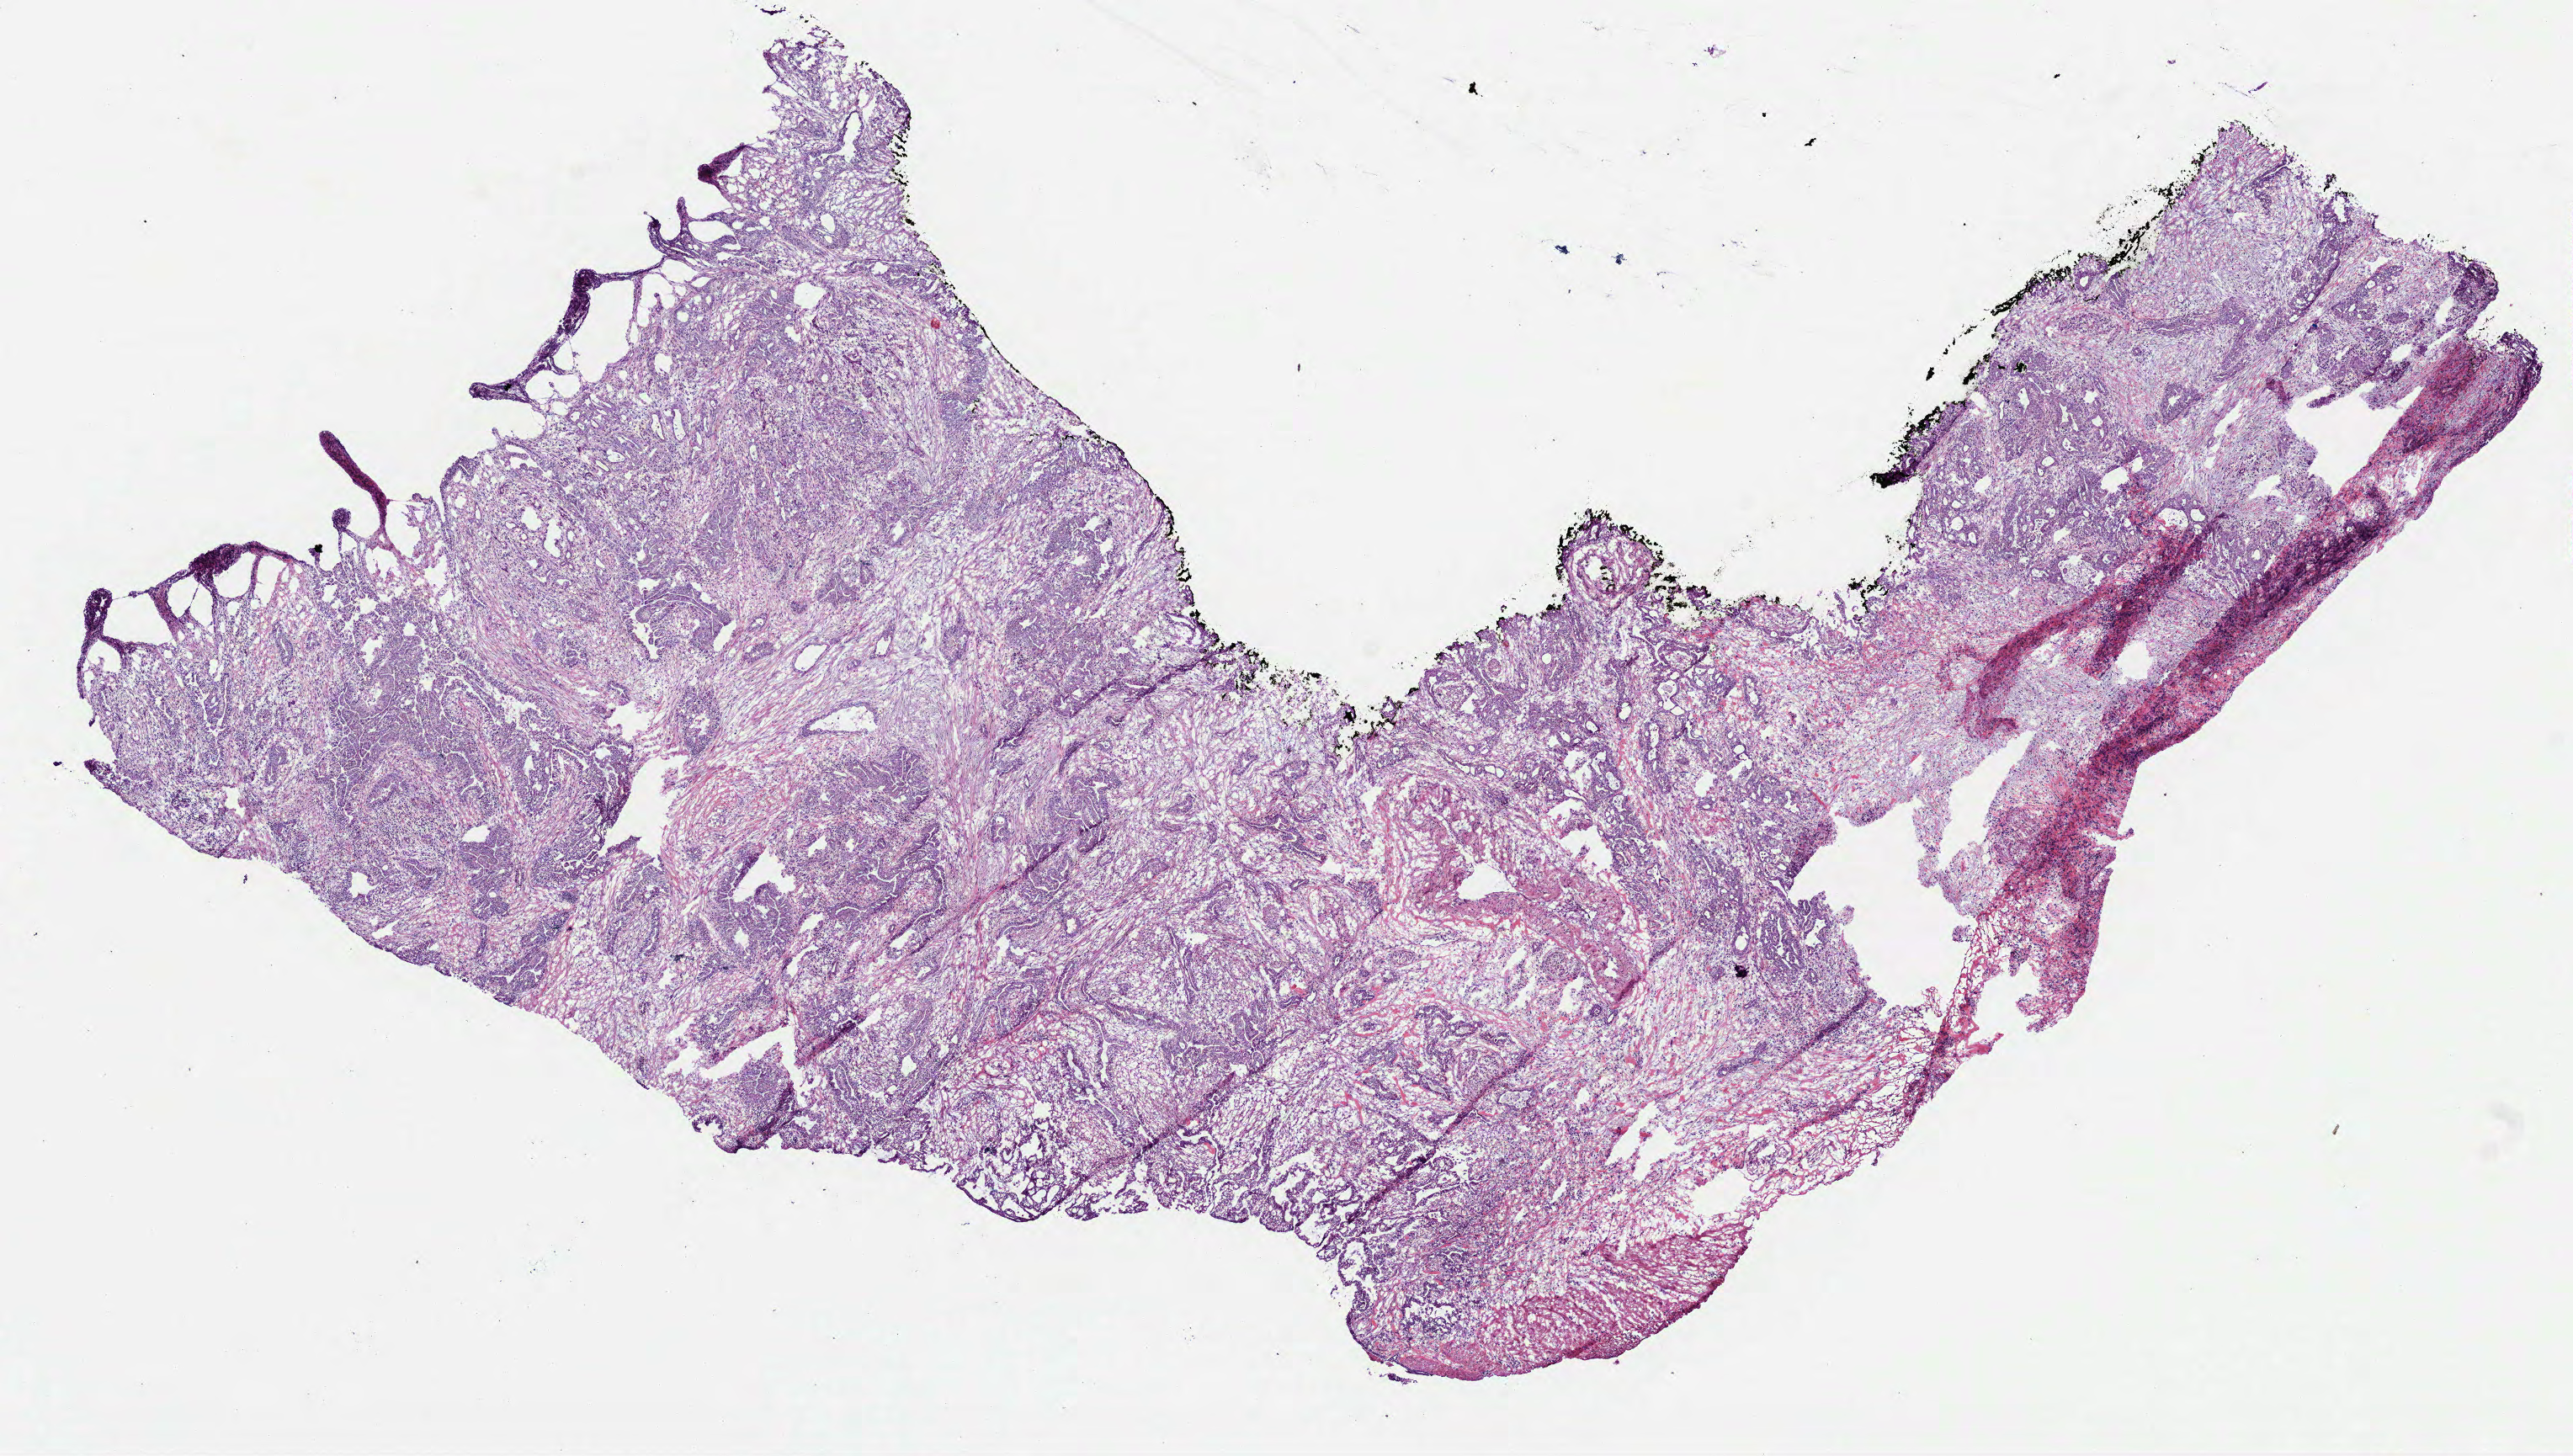
Whole-slide histology image, H&E, whole scanned area (about 12.3 x 7.0 mm) shown as a low-resolution overview. Frozen section from the bottom of the tissue portion. Primary tumour sample from the pancreas. Female patient; age at initial diagnosis 52 years. Slide review estimates, as recorded: tumour cells 75%, tumour nuclei 65%.
Histologic diagnosis: Infiltrating duct carcinoma, NOS (head of pancreas).